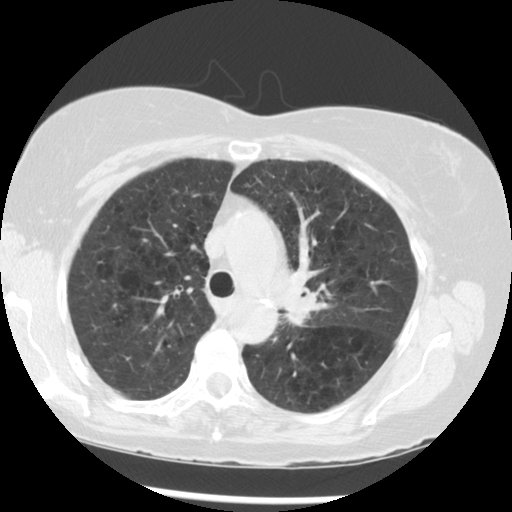
Low-dose screening chest CT, one axial slice; slice 207 of 283 in the series (ordered by position); 120 kVp; lung window (W 1500 / L -600 HU); 2.5 mm slice thickness; 512 × 512 image matrix, field of view 330 × 330 mm.
Structures marked on this image (manually delineated by an expert):
- lesion 1 (tumor, upper lobe of left lung): bounding box <285,299,325,325> (left, top, right, bottom; pixels)